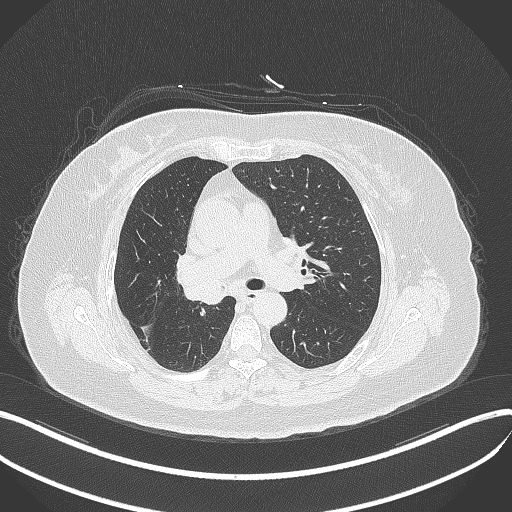
Chest CT, one axial slice; position 219 of 376 along the scan axis; 120 kVp; lung window (W 1500 / L -600 HU); 512 × 512 image matrix. Female patient, age 60 years. Case-level facts recorded for this patient, not image findings: clinical TNM (as recorded): T1c N0 M0; histopathological grade: G1-G2.
Outlined on this slice (bounding box drawn by a radiologist):
- lung tumour (recorded histology: squamous cell carcinoma): bounding box <179,270,227,310> (left, top, right, bottom; pixels)